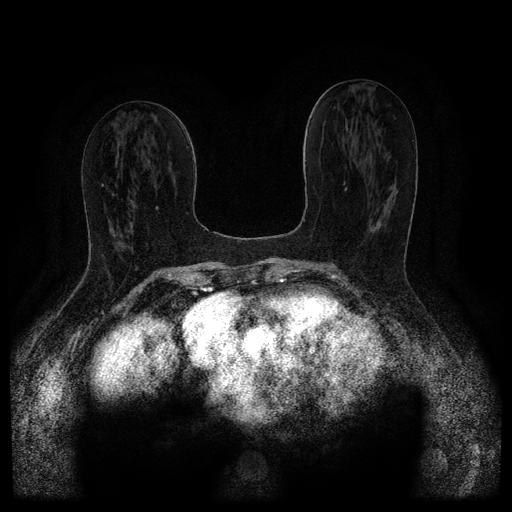
Breast MRI (dynamic contrast-enhanced, multi-phase), one axial slice; position 49 of 116 along the scan axis; dynamic contrast-enhanced series, time point 2 of 5 at this slice position (early post-contrast); 1.5 T; TE 2.6 ms, TR 5.4 ms; 2 mm slice thickness; 512 × 512 image matrix, field of view 340 × 340 mm. Patient: female, 67 years.
Annotated regions visible in this slice (semi-automatic segmentation, software-assisted and operator-edited):
- breast lesion (labelled 'tumour' in the annotation; benign lesions carry a separate 'benign' label): box from (x=368, y=221) to (x=383, y=233) px